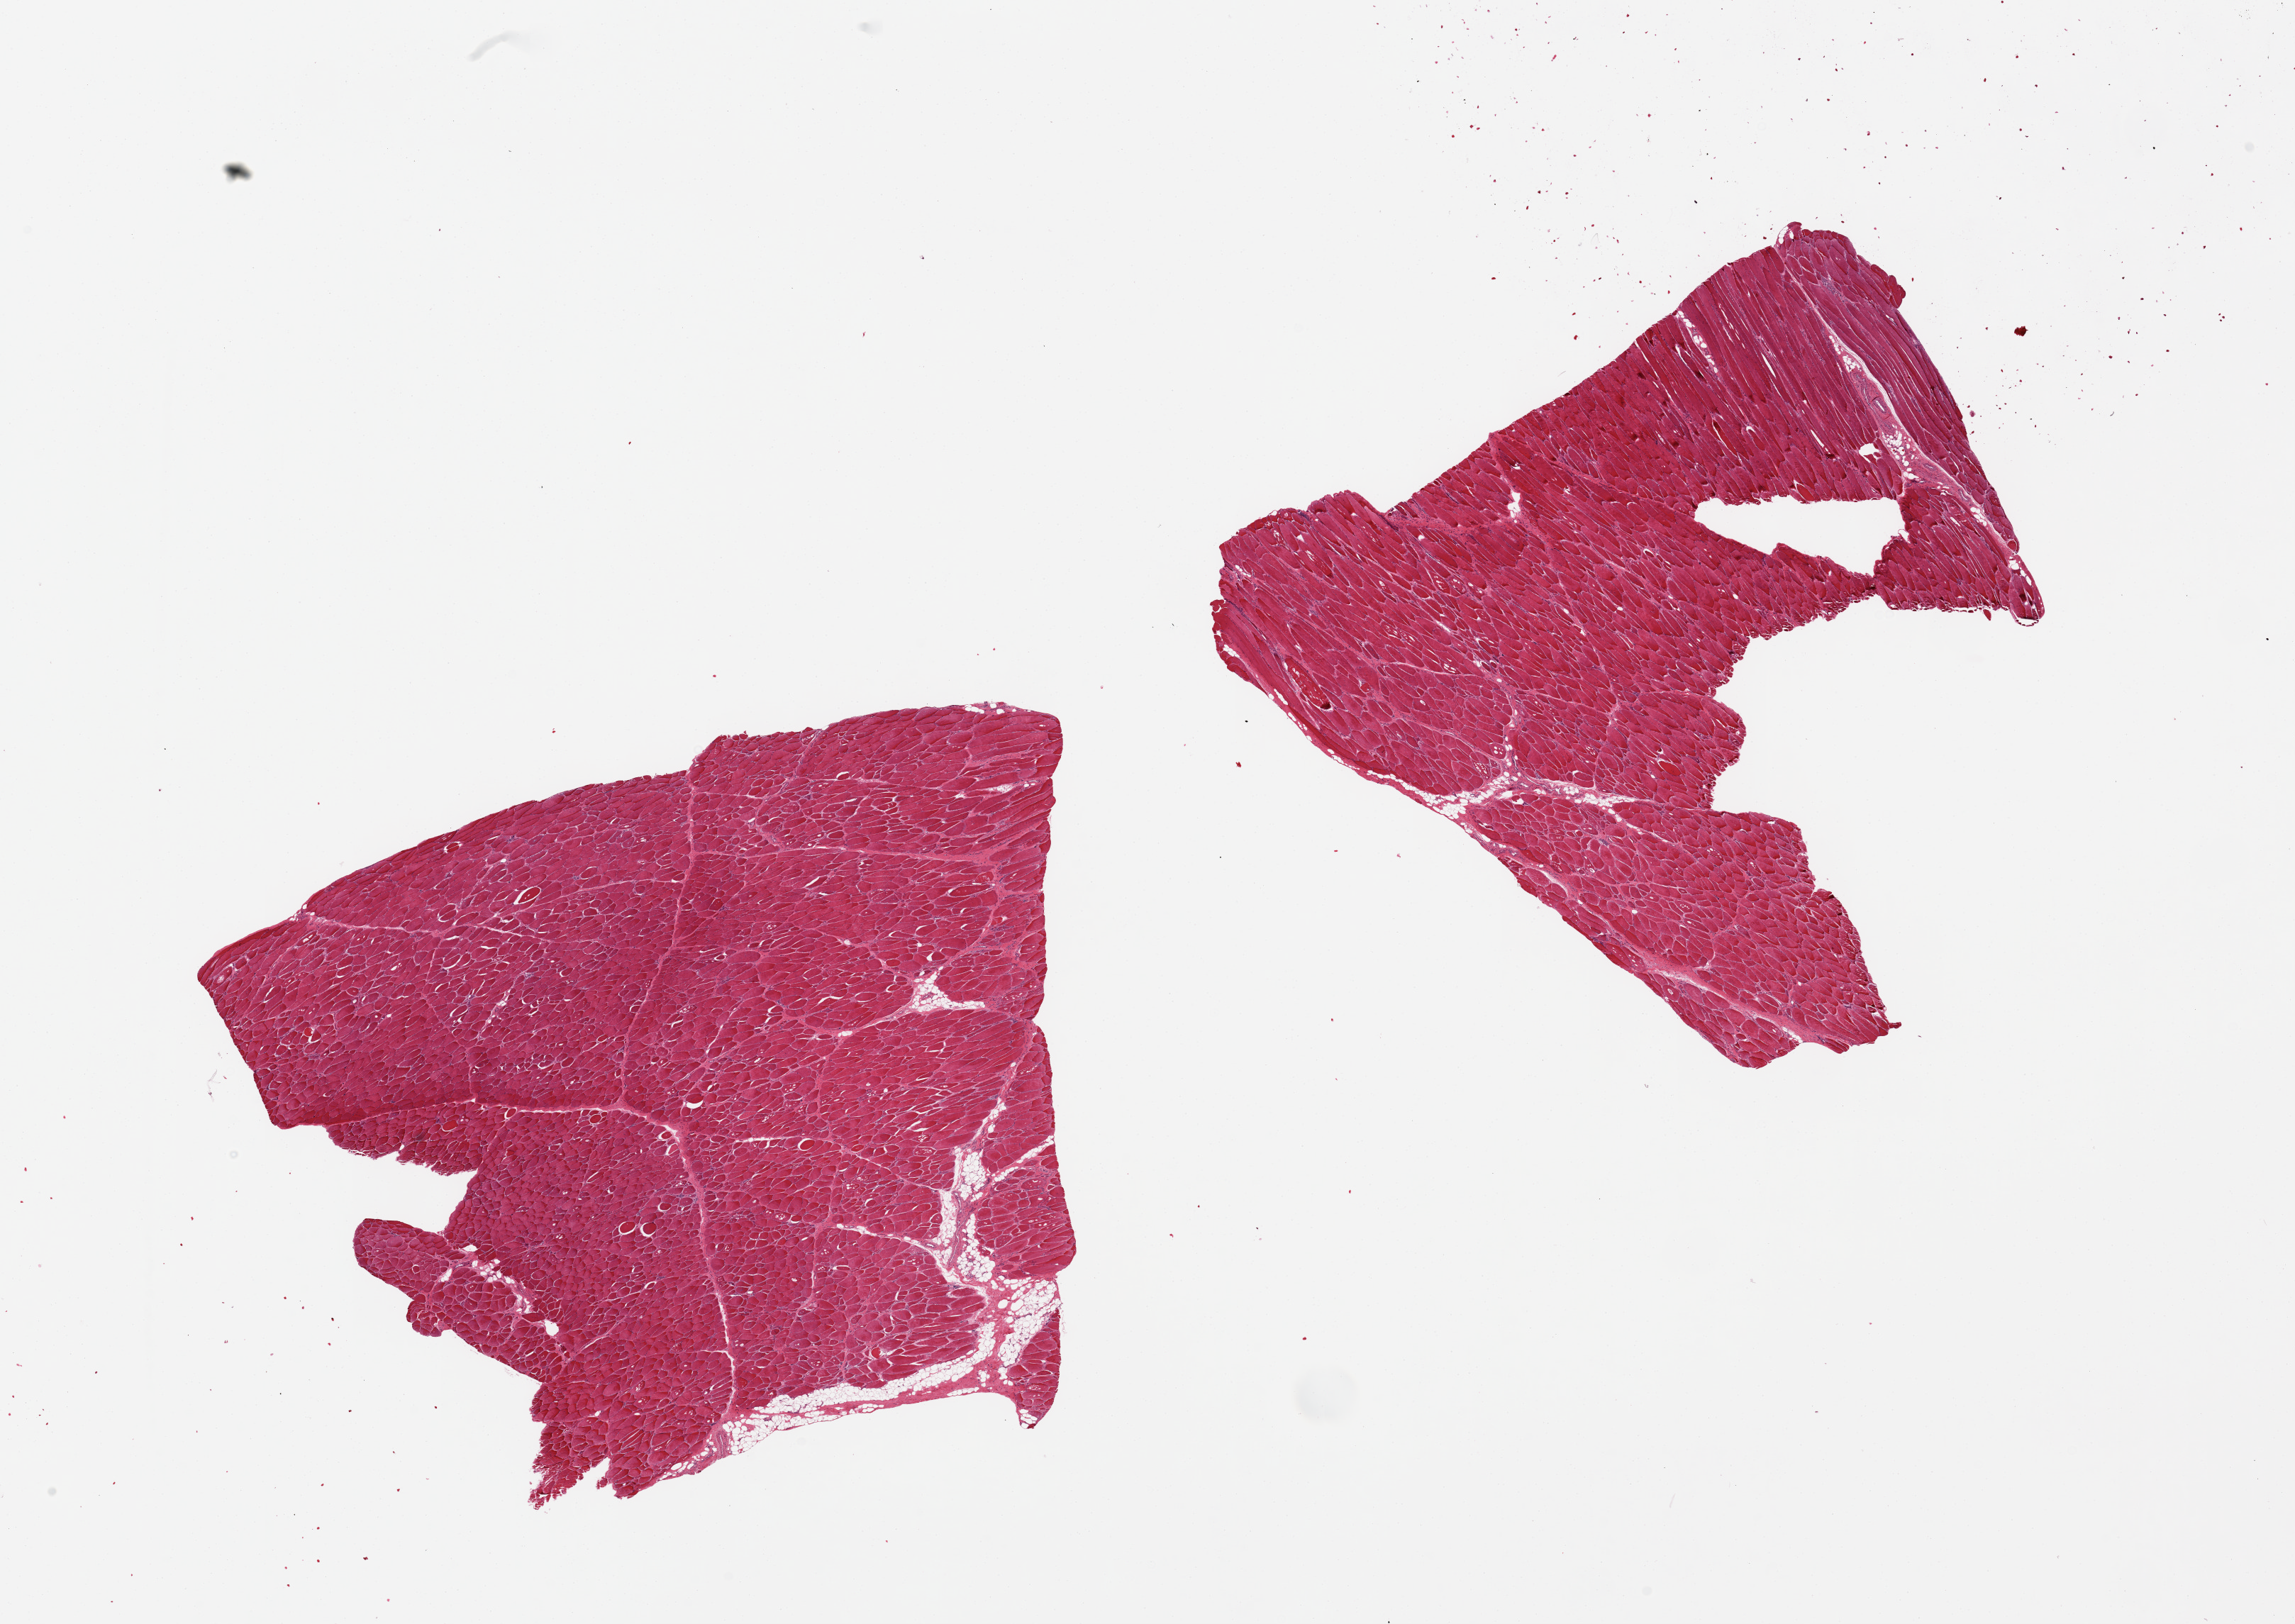
Whole-slide image, haematoxylin and eosin stain, low-resolution overview of the scanned area, about 25.6 x 18.1 mm (from a 20x scan), PAXgene-fixed, paraffin-embedded tissue, sampled site (target tissue): skeletal muscle, donor tissue sample.
Reviewer comment on this tissue sample: 2 pieces, ~10% interstitial fat.